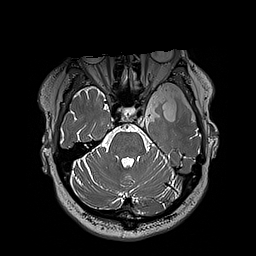
Brain MRI from a brain-tumour surgery series, one axial slice; position 141 of 192 along the scan axis; 1 mm slice thickness; 256 × 256 image matrix, field of view 250 × 250 mm. From the clinical record (not read from this slice): histopathology: Oligodendroglioma; WHO grade: 3; IDH mutation: yes; tumour location: Left Sylvian Fissure (Temporal).
Structures marked on this image (expert manual segmentation):
- tumour: bounding box (x1, y1, x2, y2) in pixels: (125, 70, 197, 120)